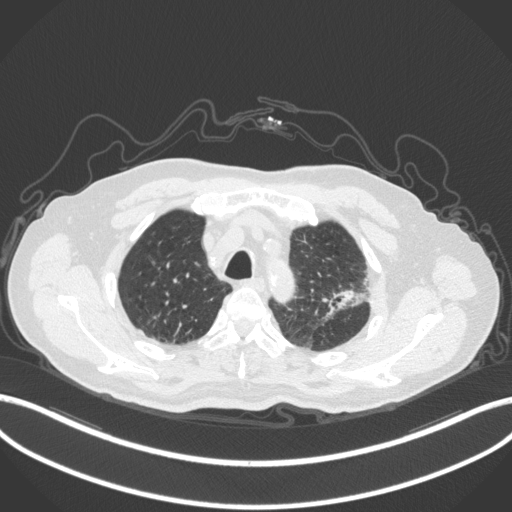
Chest CT, one axial slice. Position 245 of 331 along the scan axis. Reconstruction kernel B31f. 120 kVp. Lung window (W 1500 / L -600 HU). 1 mm slice thickness. 512 × 512 image matrix. Patient: male, 79 years. Case-level facts recorded for this patient, not image findings: clinical TNM (as recorded): T2a N1 M1; histopathological grade: G3.
Outlined on this slice (rectangle marked by the reading radiologist):
- lung tumour (recorded histology: adenocarcinoma): bounding box (x1, y1, x2, y2) in pixels: (319, 284, 372, 322)